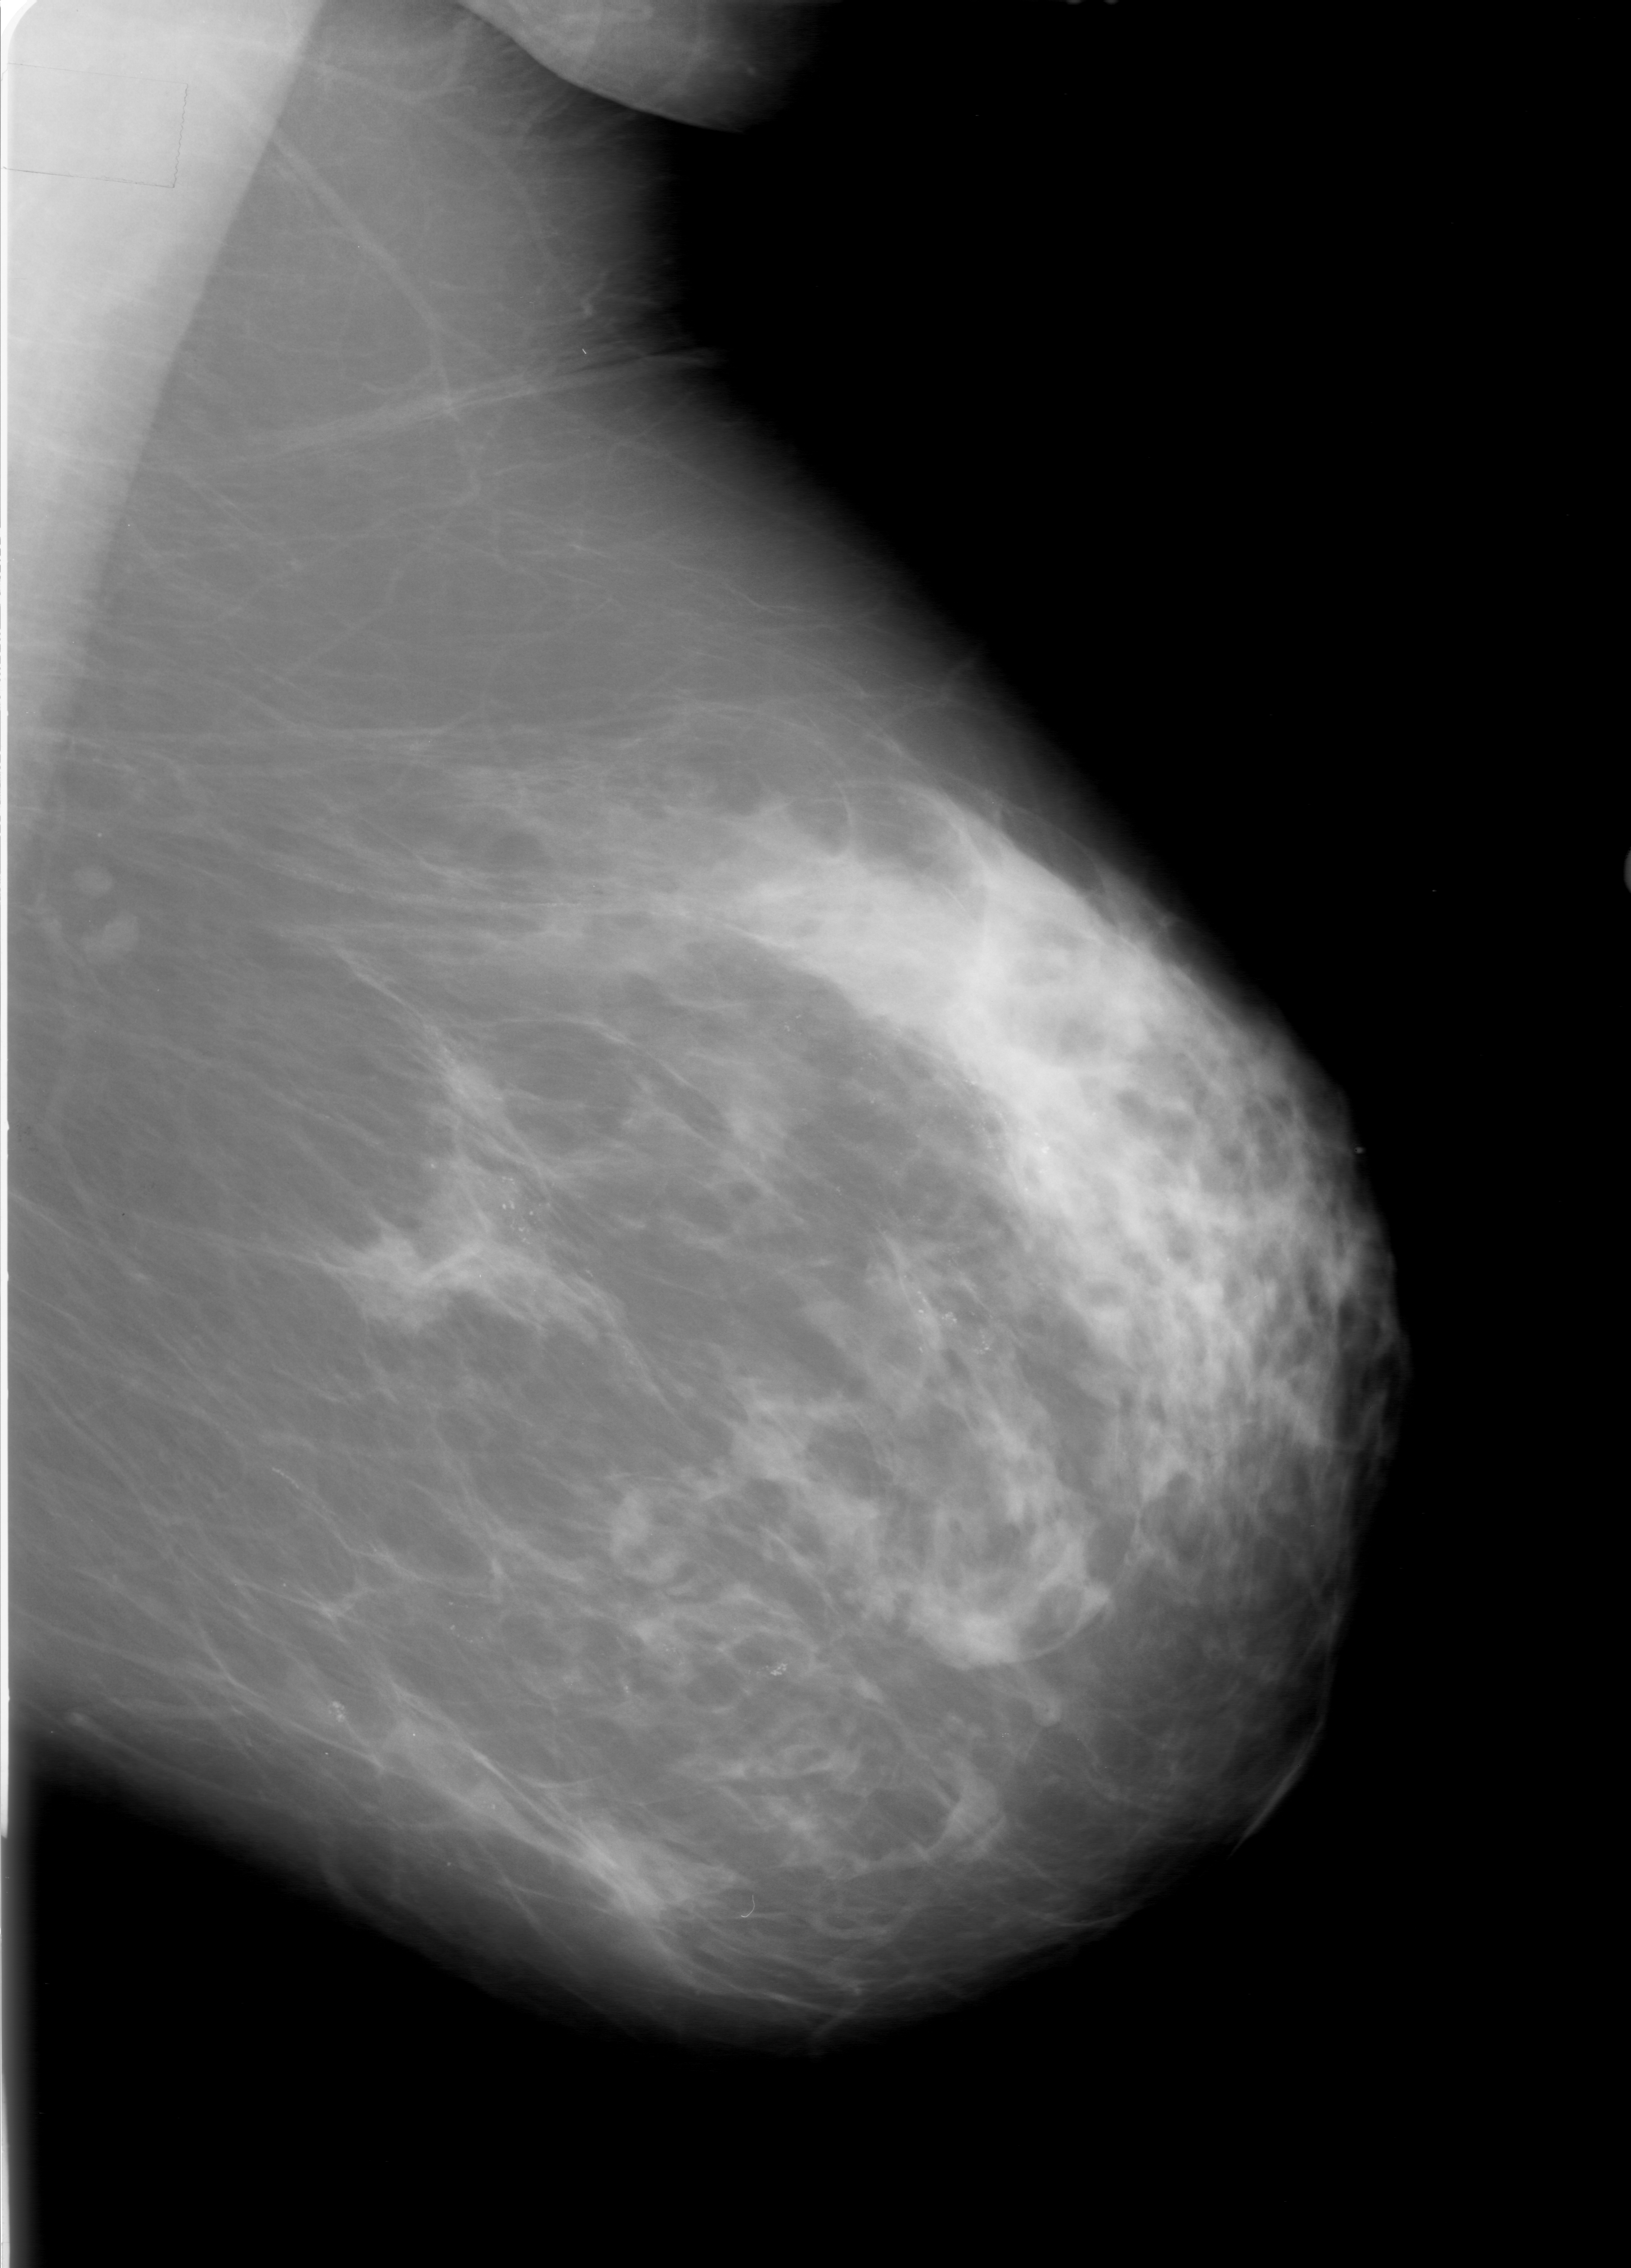
Digitized screen-film mammogram. Left breast. MLO view. Breast composition: heterogeneously dense (BI-RADS density category 3 of 4). 1631 × 2268 image matrix.
Marked abnormalities (boxes around the expert regions of interest):
- calcifications, morphology pleomorphic, distribution regional; BI-RADS assessment category 5; subtlety rating 5 on a 1 (subtle) to 5 (obvious) scale; pathology result (as recorded, not read from the image): malignant: bounding box (x1, y1, x2, y2) in pixels: (333, 806, 1153, 1446)